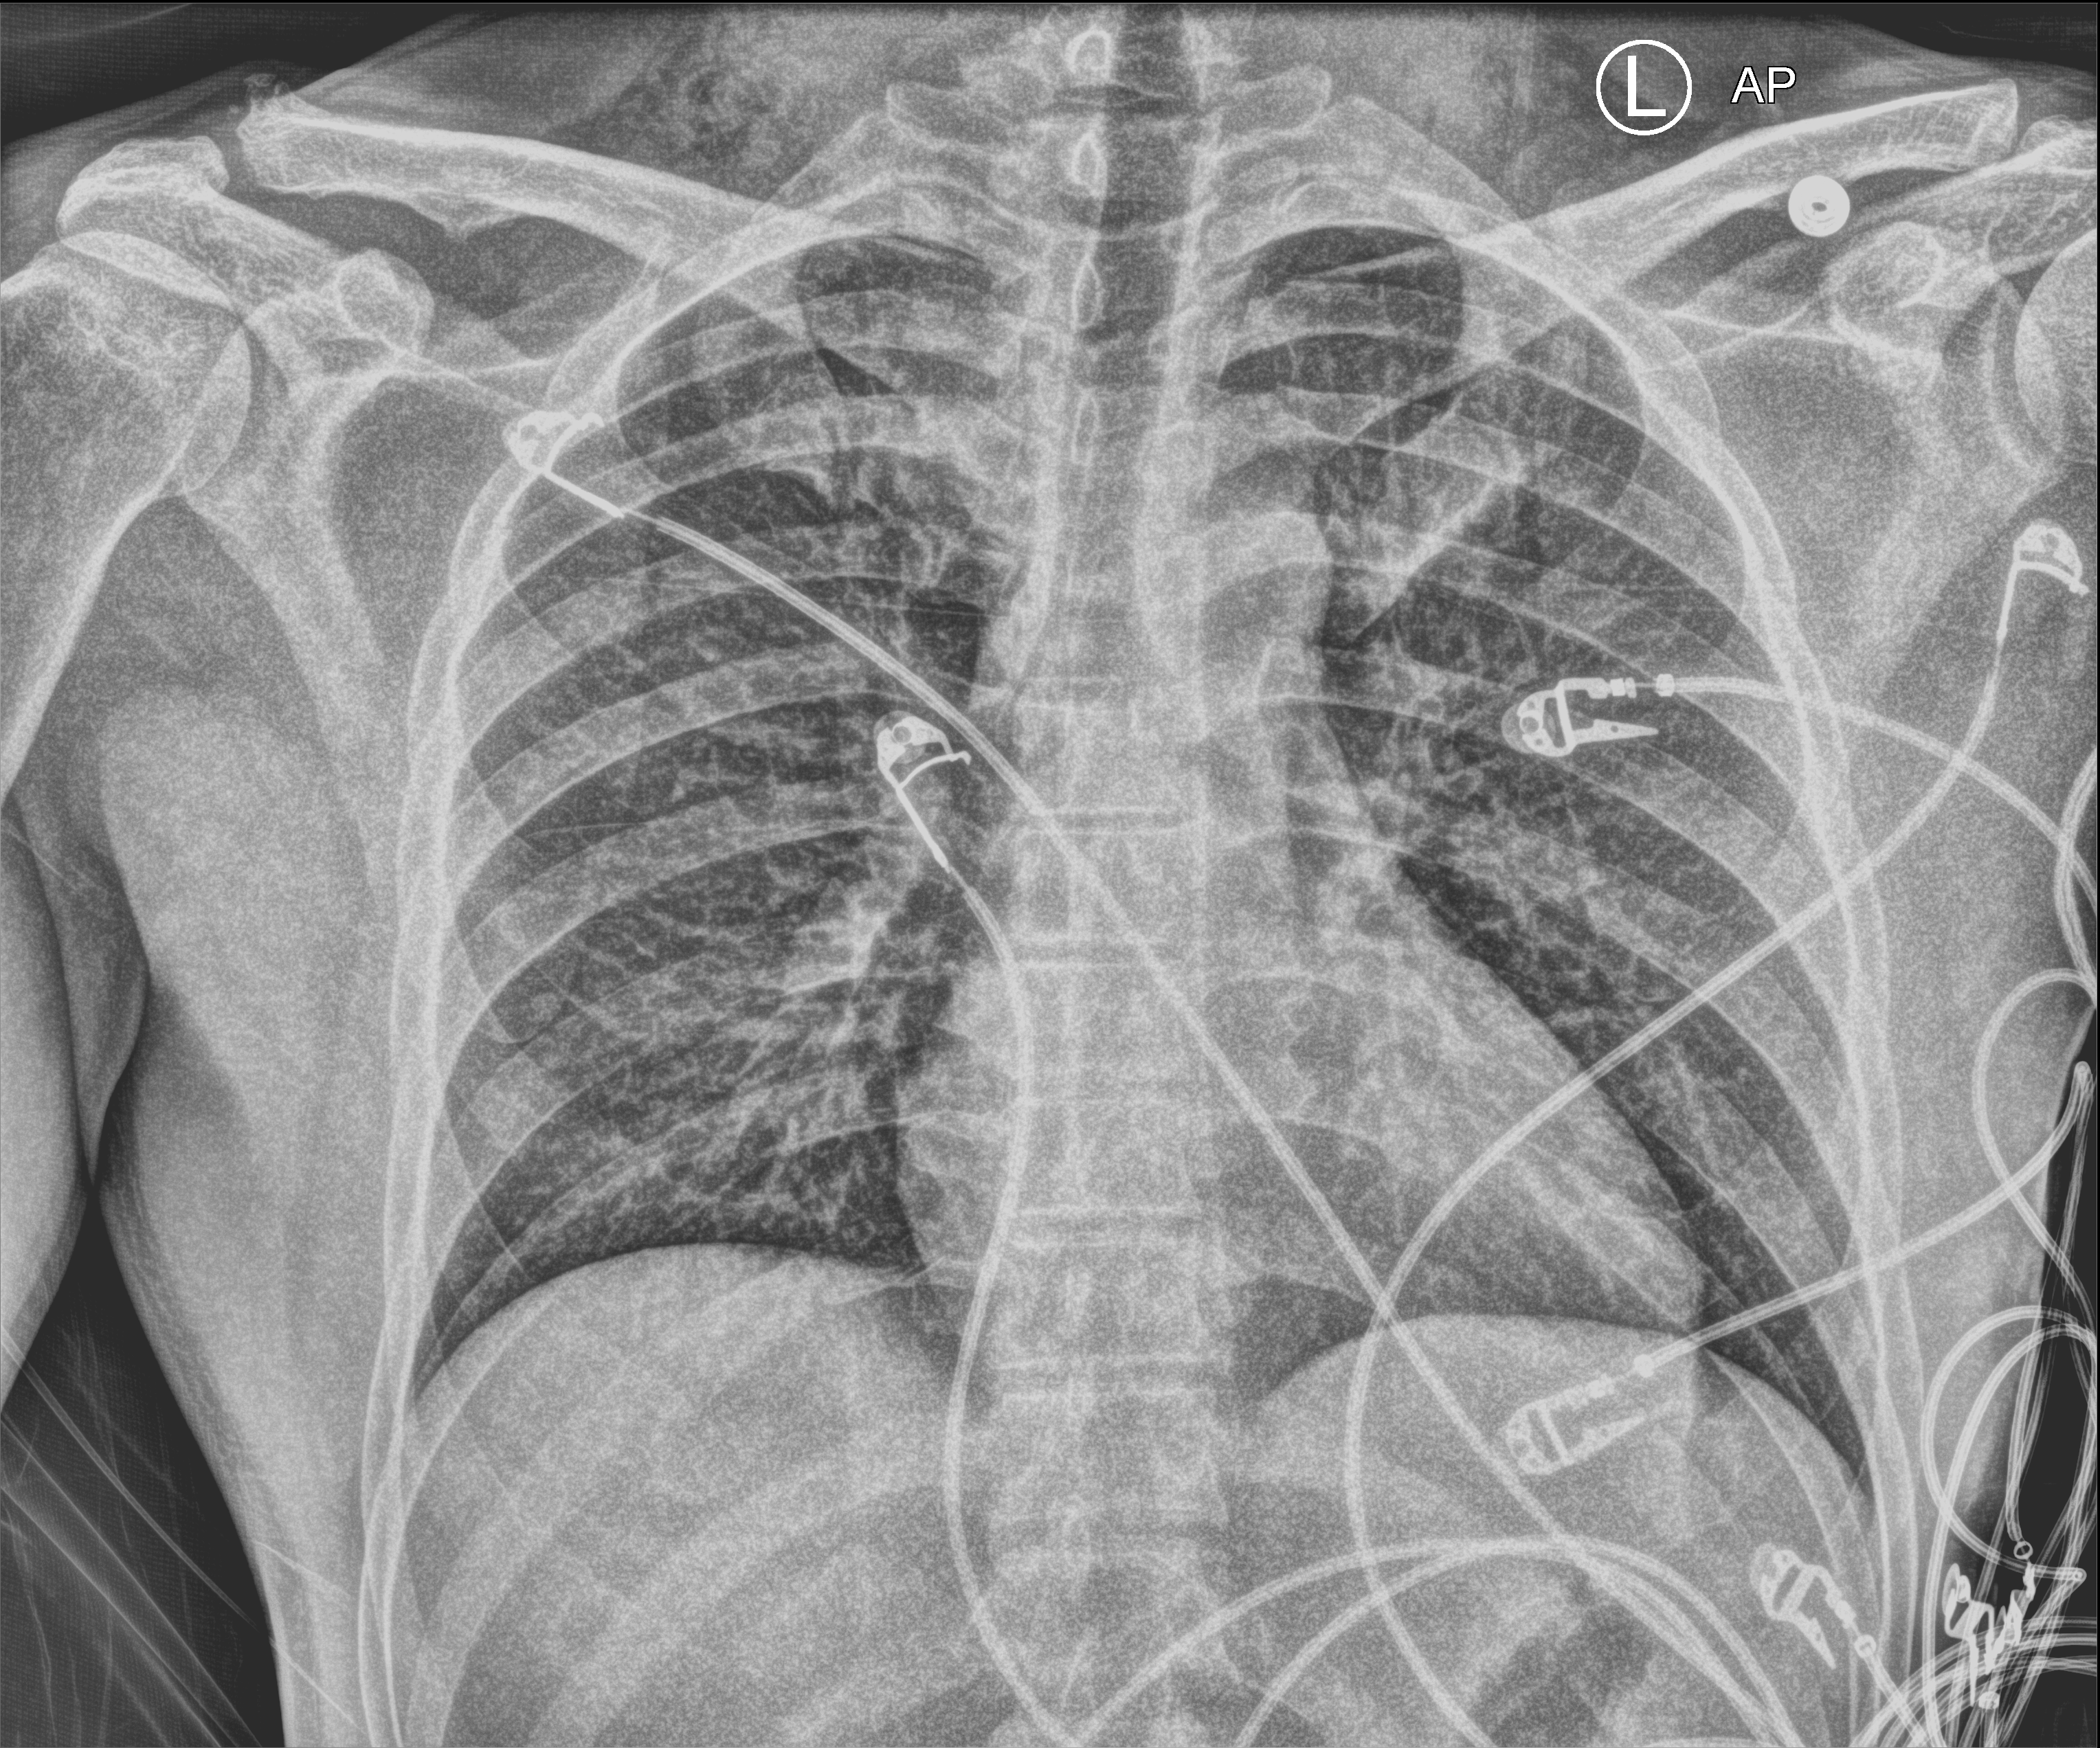
Bedside chest radiograph (computed radiography). Patient hospitalised with COVID-19; male, aged 18–59 years.
Admission-level facts for this patient (not findings on this image; timing relative to this image not recorded):
- COPD (admission record): no
- diabetes (admission record): no